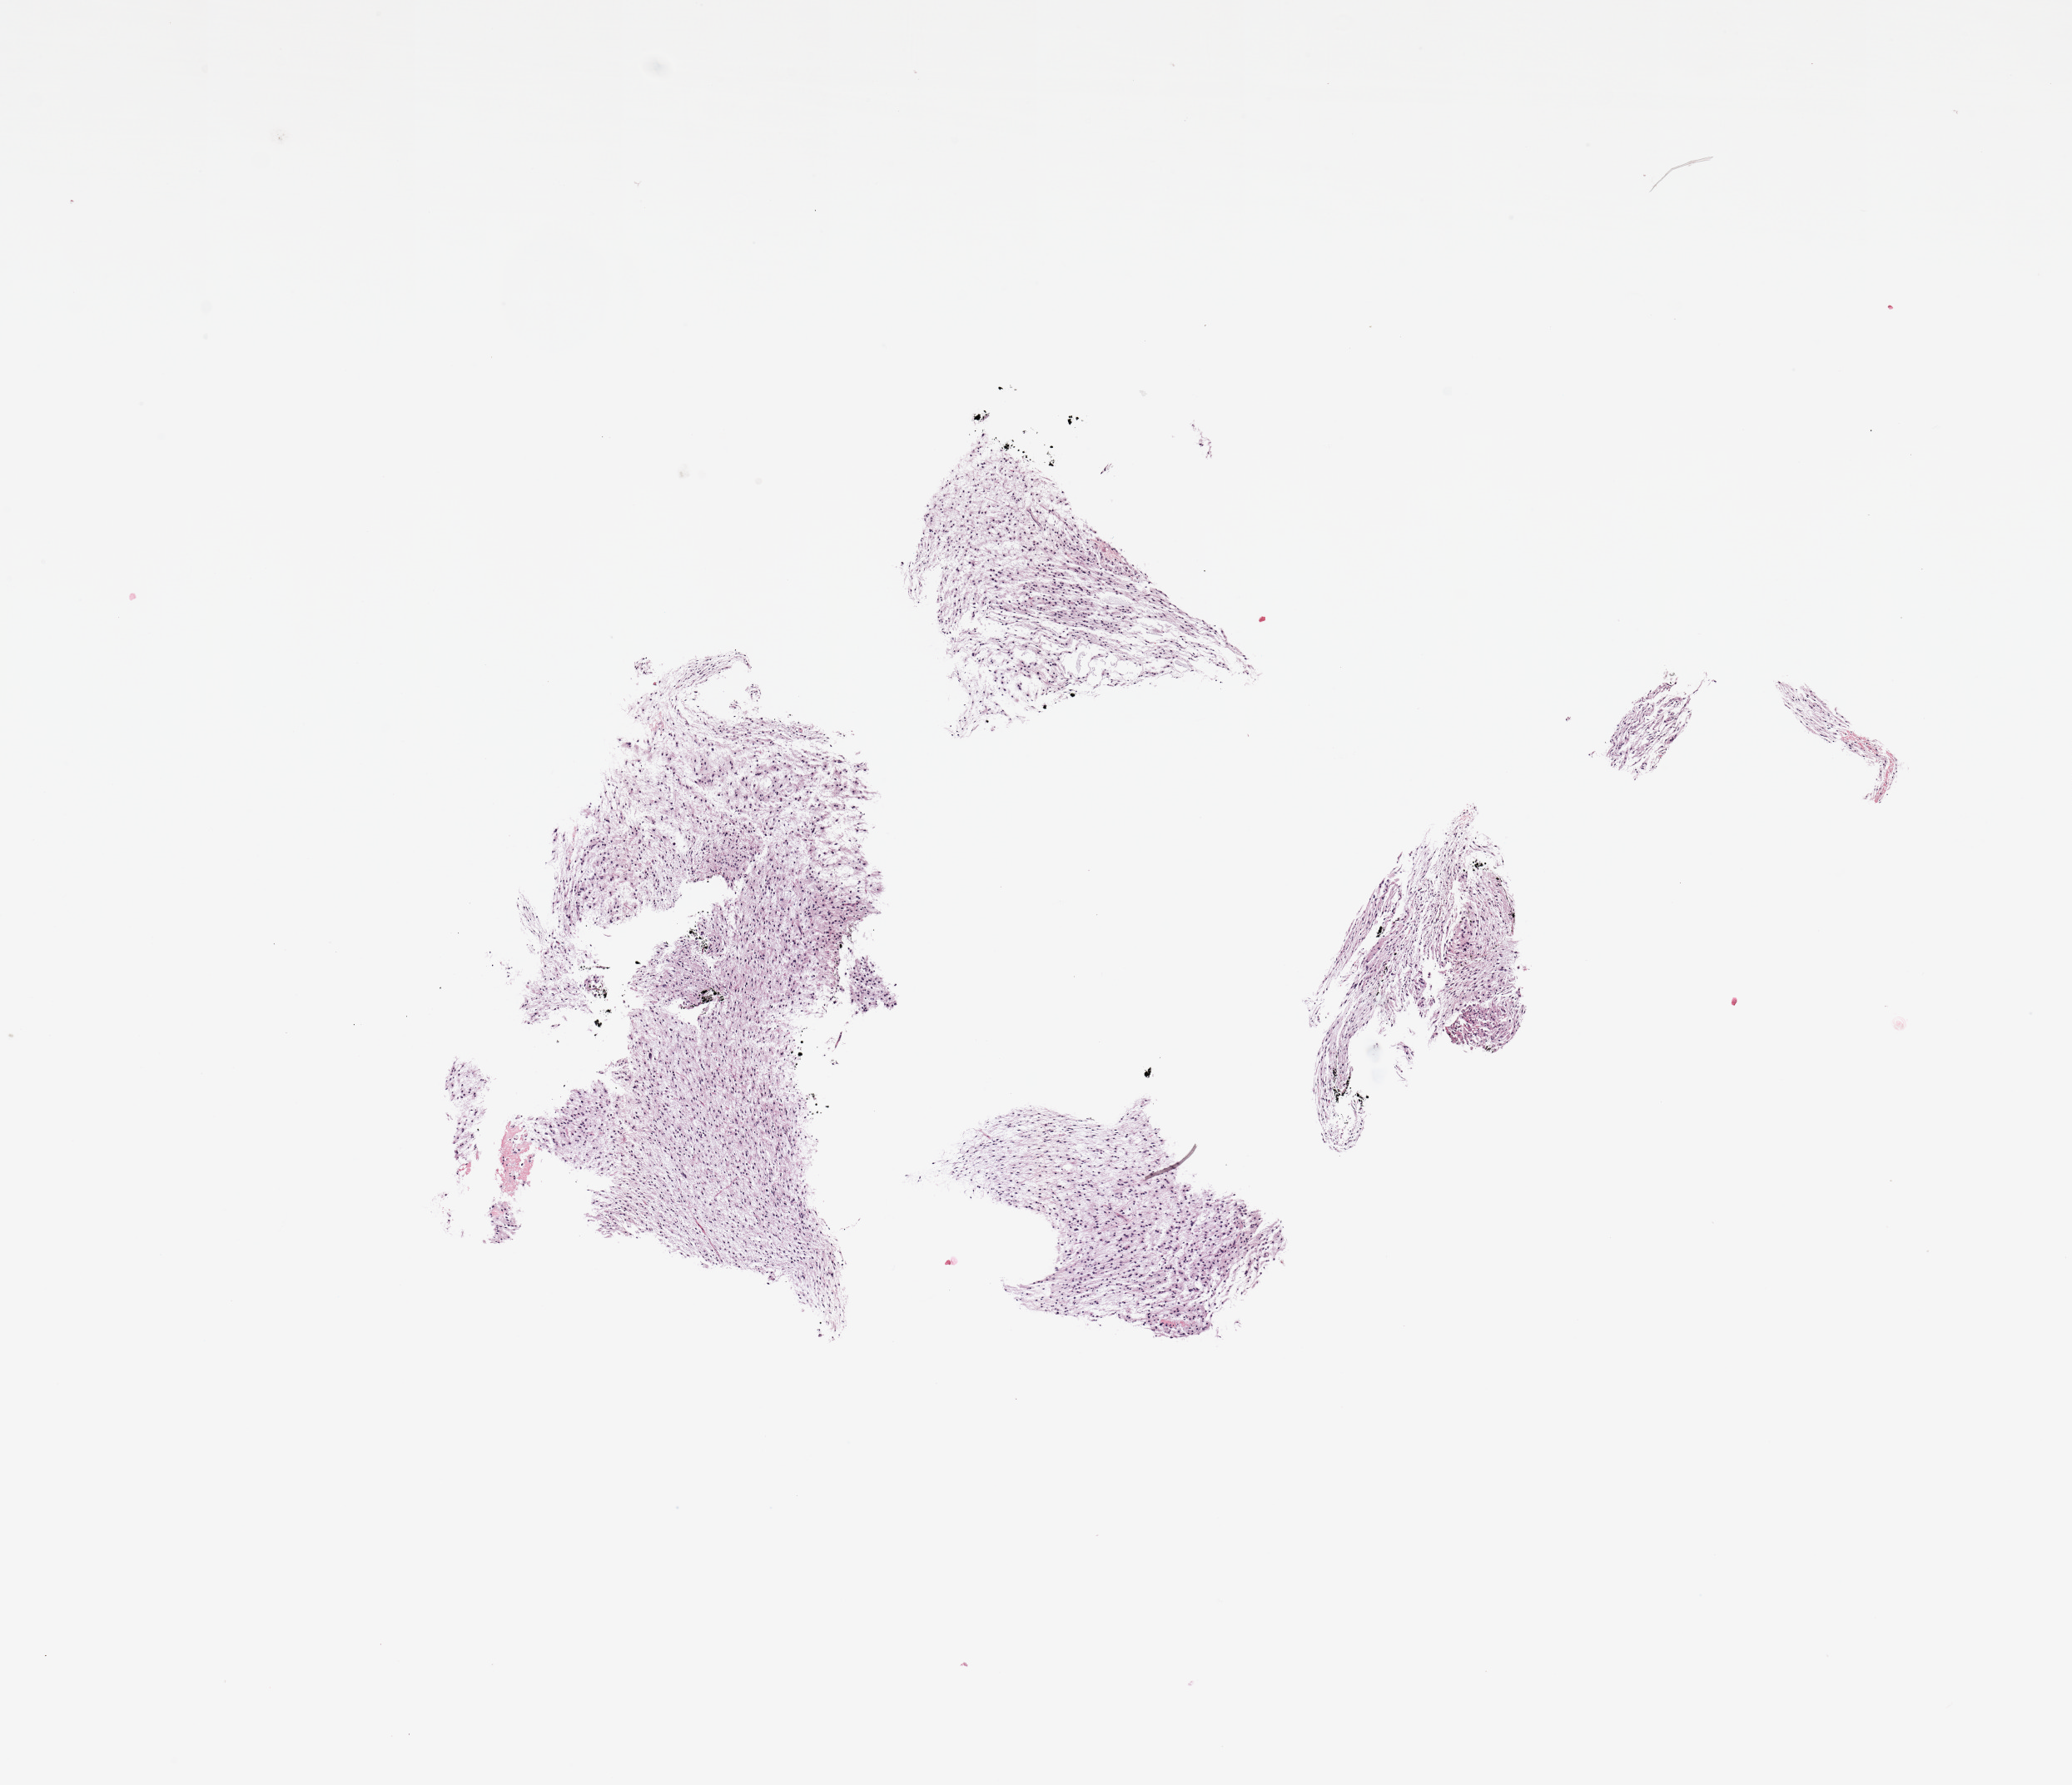
Whole-slide histology image, Hematoxylin and eosin (H&E) stained — low-resolution overview of the scanned area, about 9.8 x 8.5 mm (acquisition: 20x scan). Tumour tissue sample, sampled site: frontal lobe. Male, 34 y/o. Slide review estimates, as recorded: tumour nuclei 85%, necrosis 3%.
Histologic diagnosis: Glioblastoma. Primary tumour site (as recorded): frontal lobe.